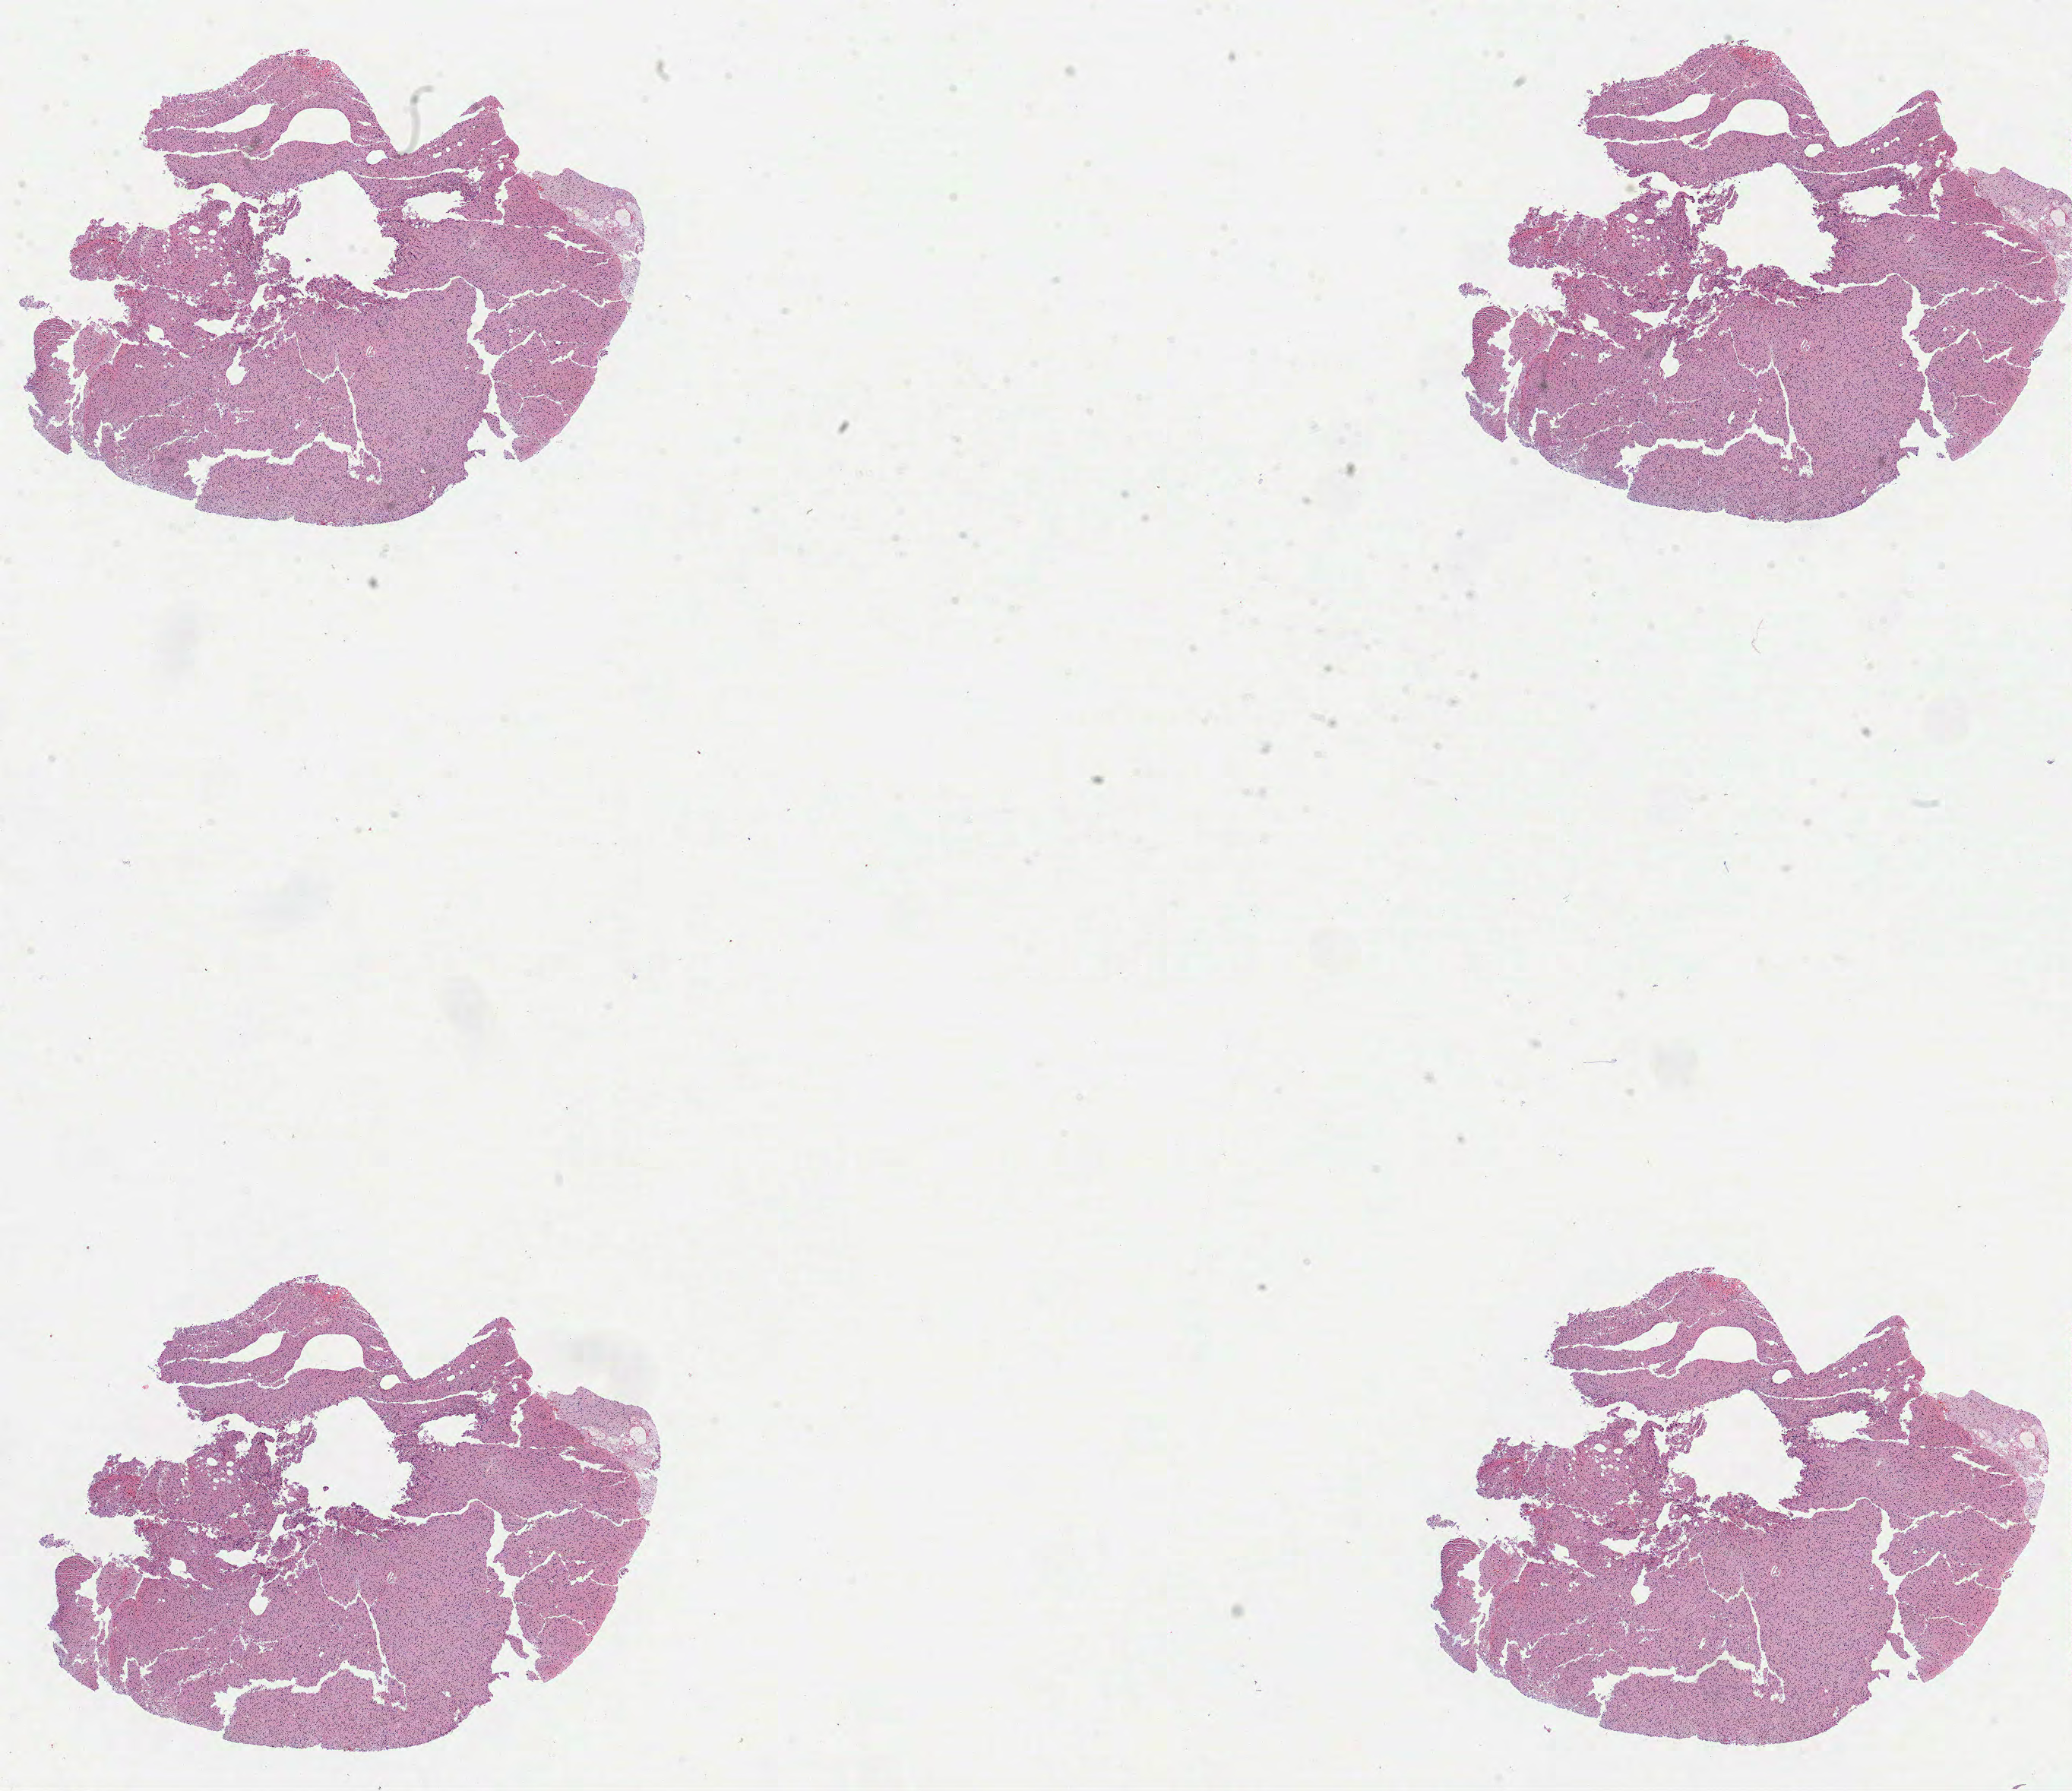
H&E whole-slide image, low-resolution overview of the scanned area, about 22.0 x 19.0 mm (from a 40x scan); formalin-fixed paraffin-embedded (FFPE) diagnostic section; primary tumour sample from the brain. Female, age 23 years at initial diagnosis. Histologic grade: G3 (poorly differentiated).
Diagnosis: Oligodendroglioma, anaplastic (cerebrum).